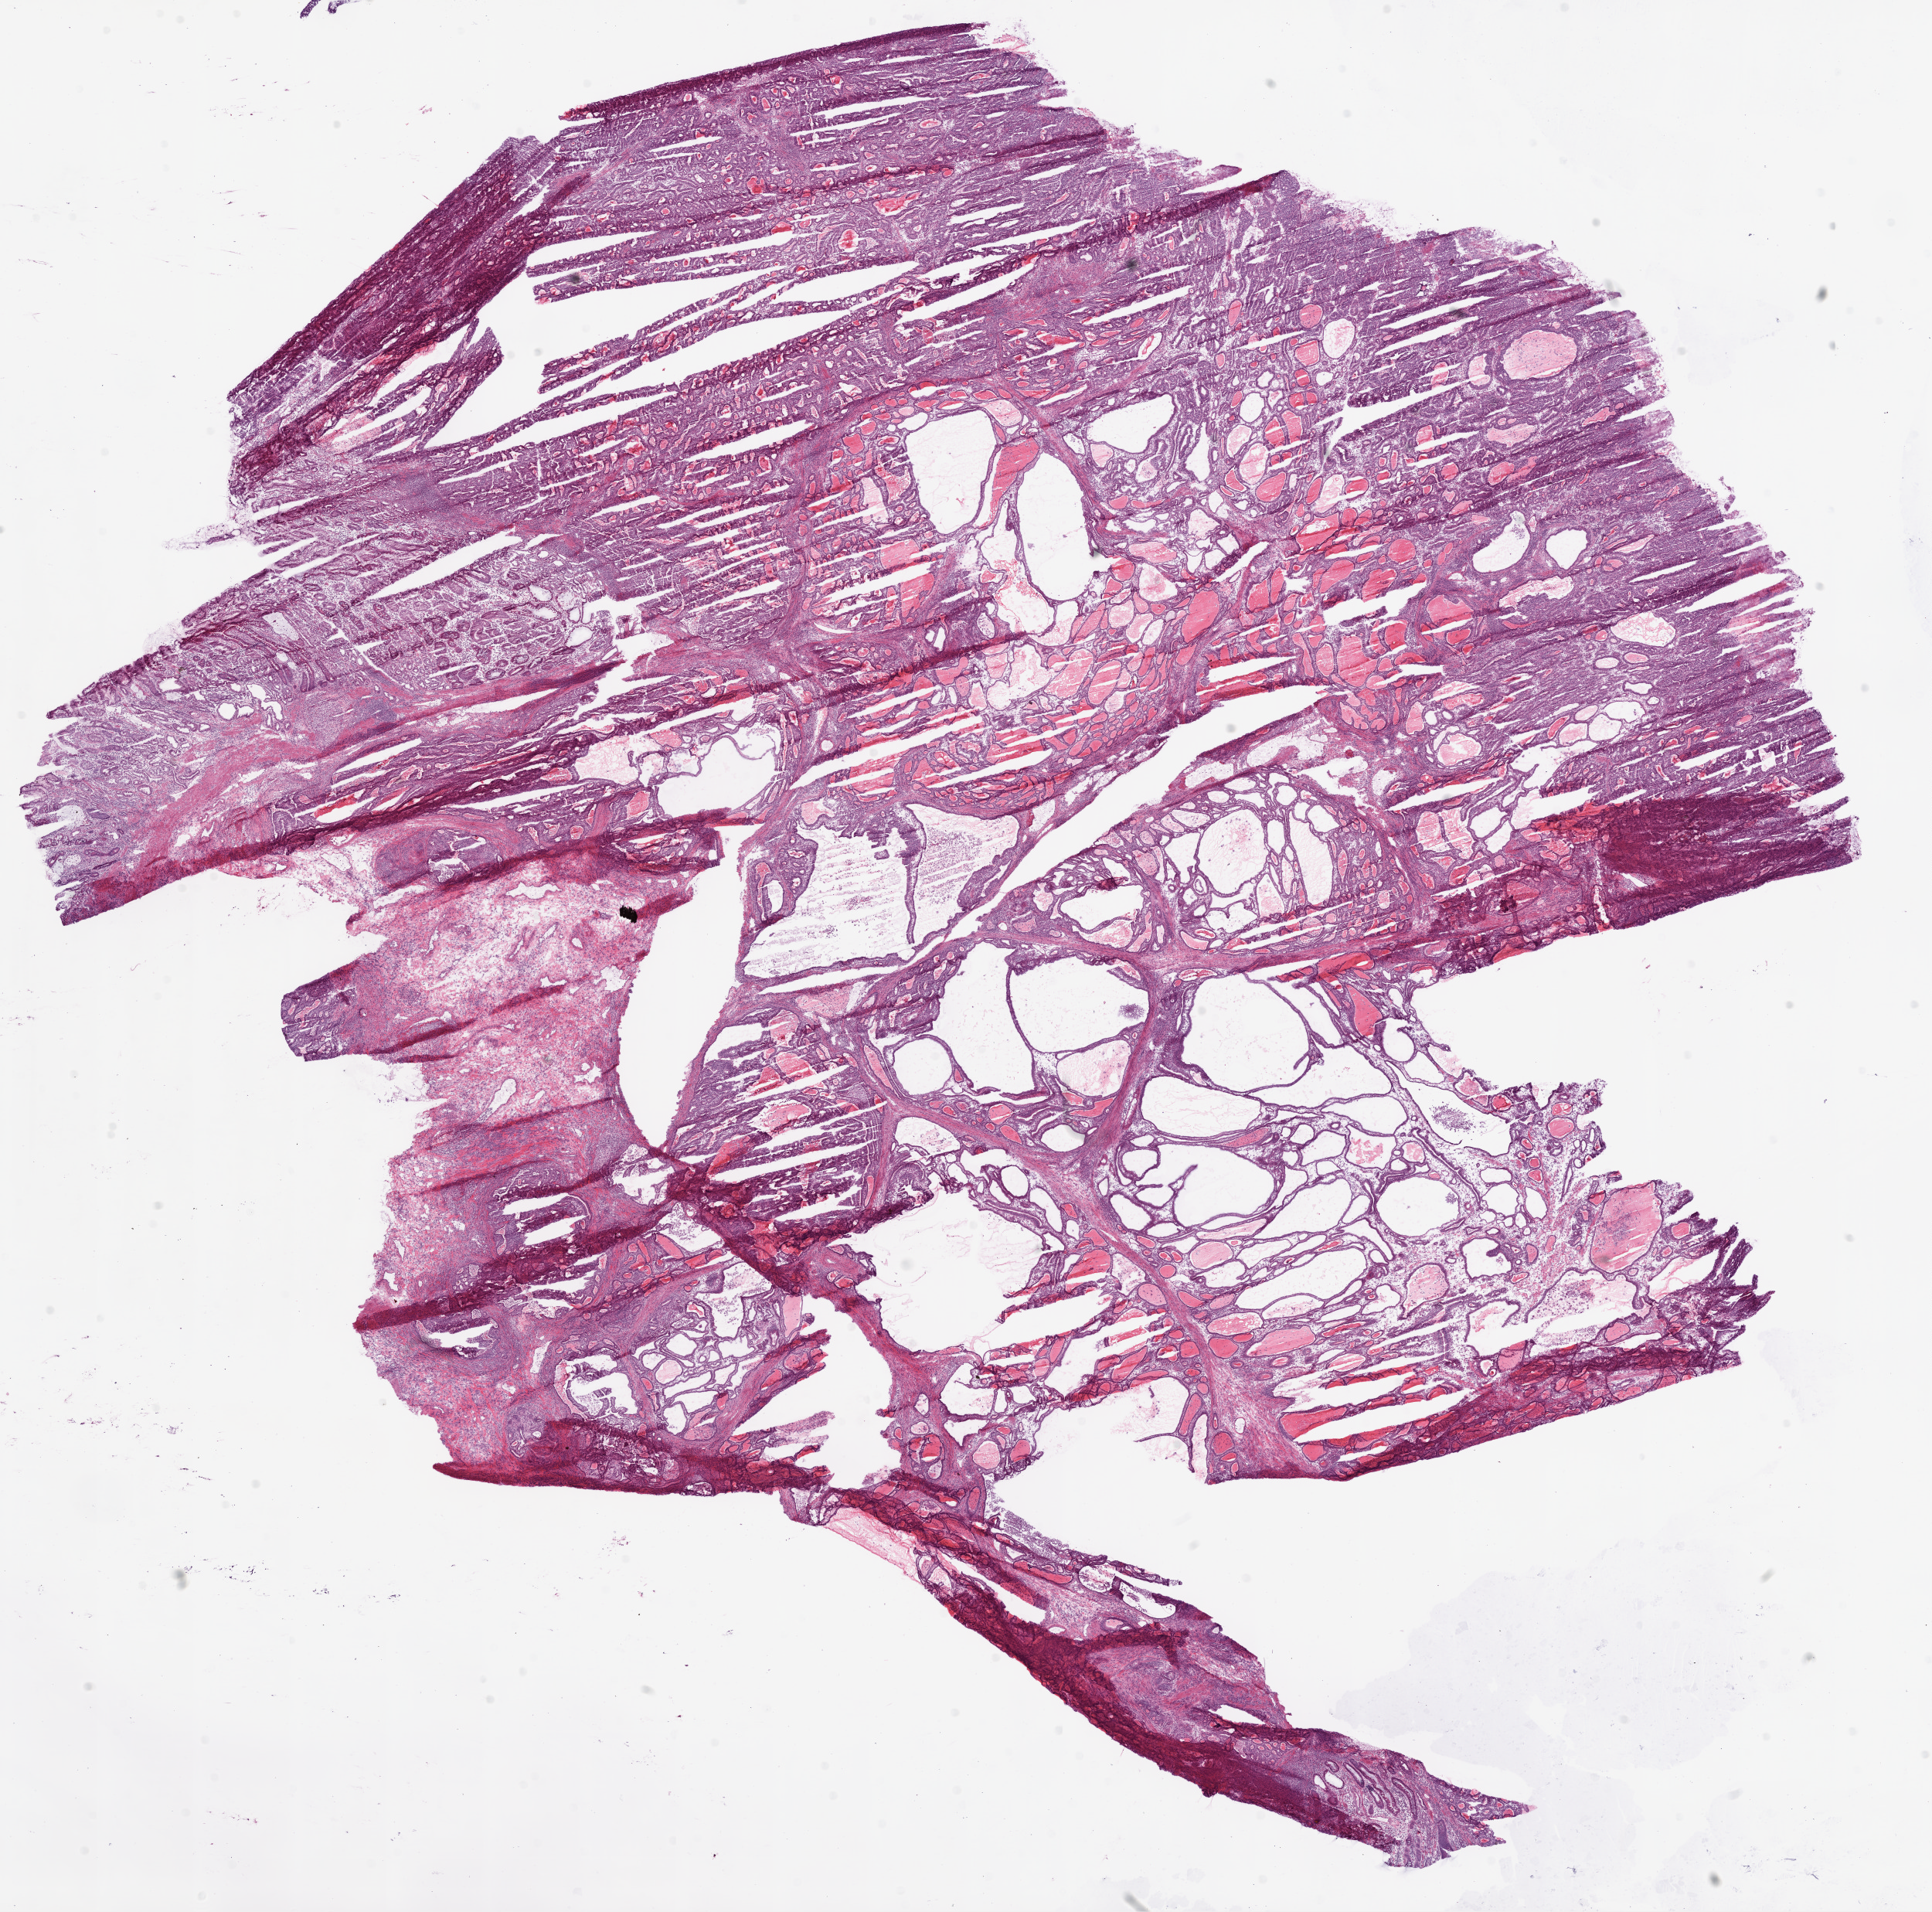
H&E-stained whole-slide image — shown as a low-resolution overview of the whole scanned area (about 20.1 x 19.9 mm), frozen section, sample: primary tumour, stomach. Male patient; age at initial diagnosis 72 years. Histologic grade: G2 (moderately differentiated). Composition of this section per pathologist review: tumour cells 91%, tumour nuclei 85%, normal cells 2%, stromal cells 5%, necrosis 2%.
* pathologic diagnosis: Adenocarcinoma, NOS
* lymph nodes positive (case pathology): 3 of 8 examined